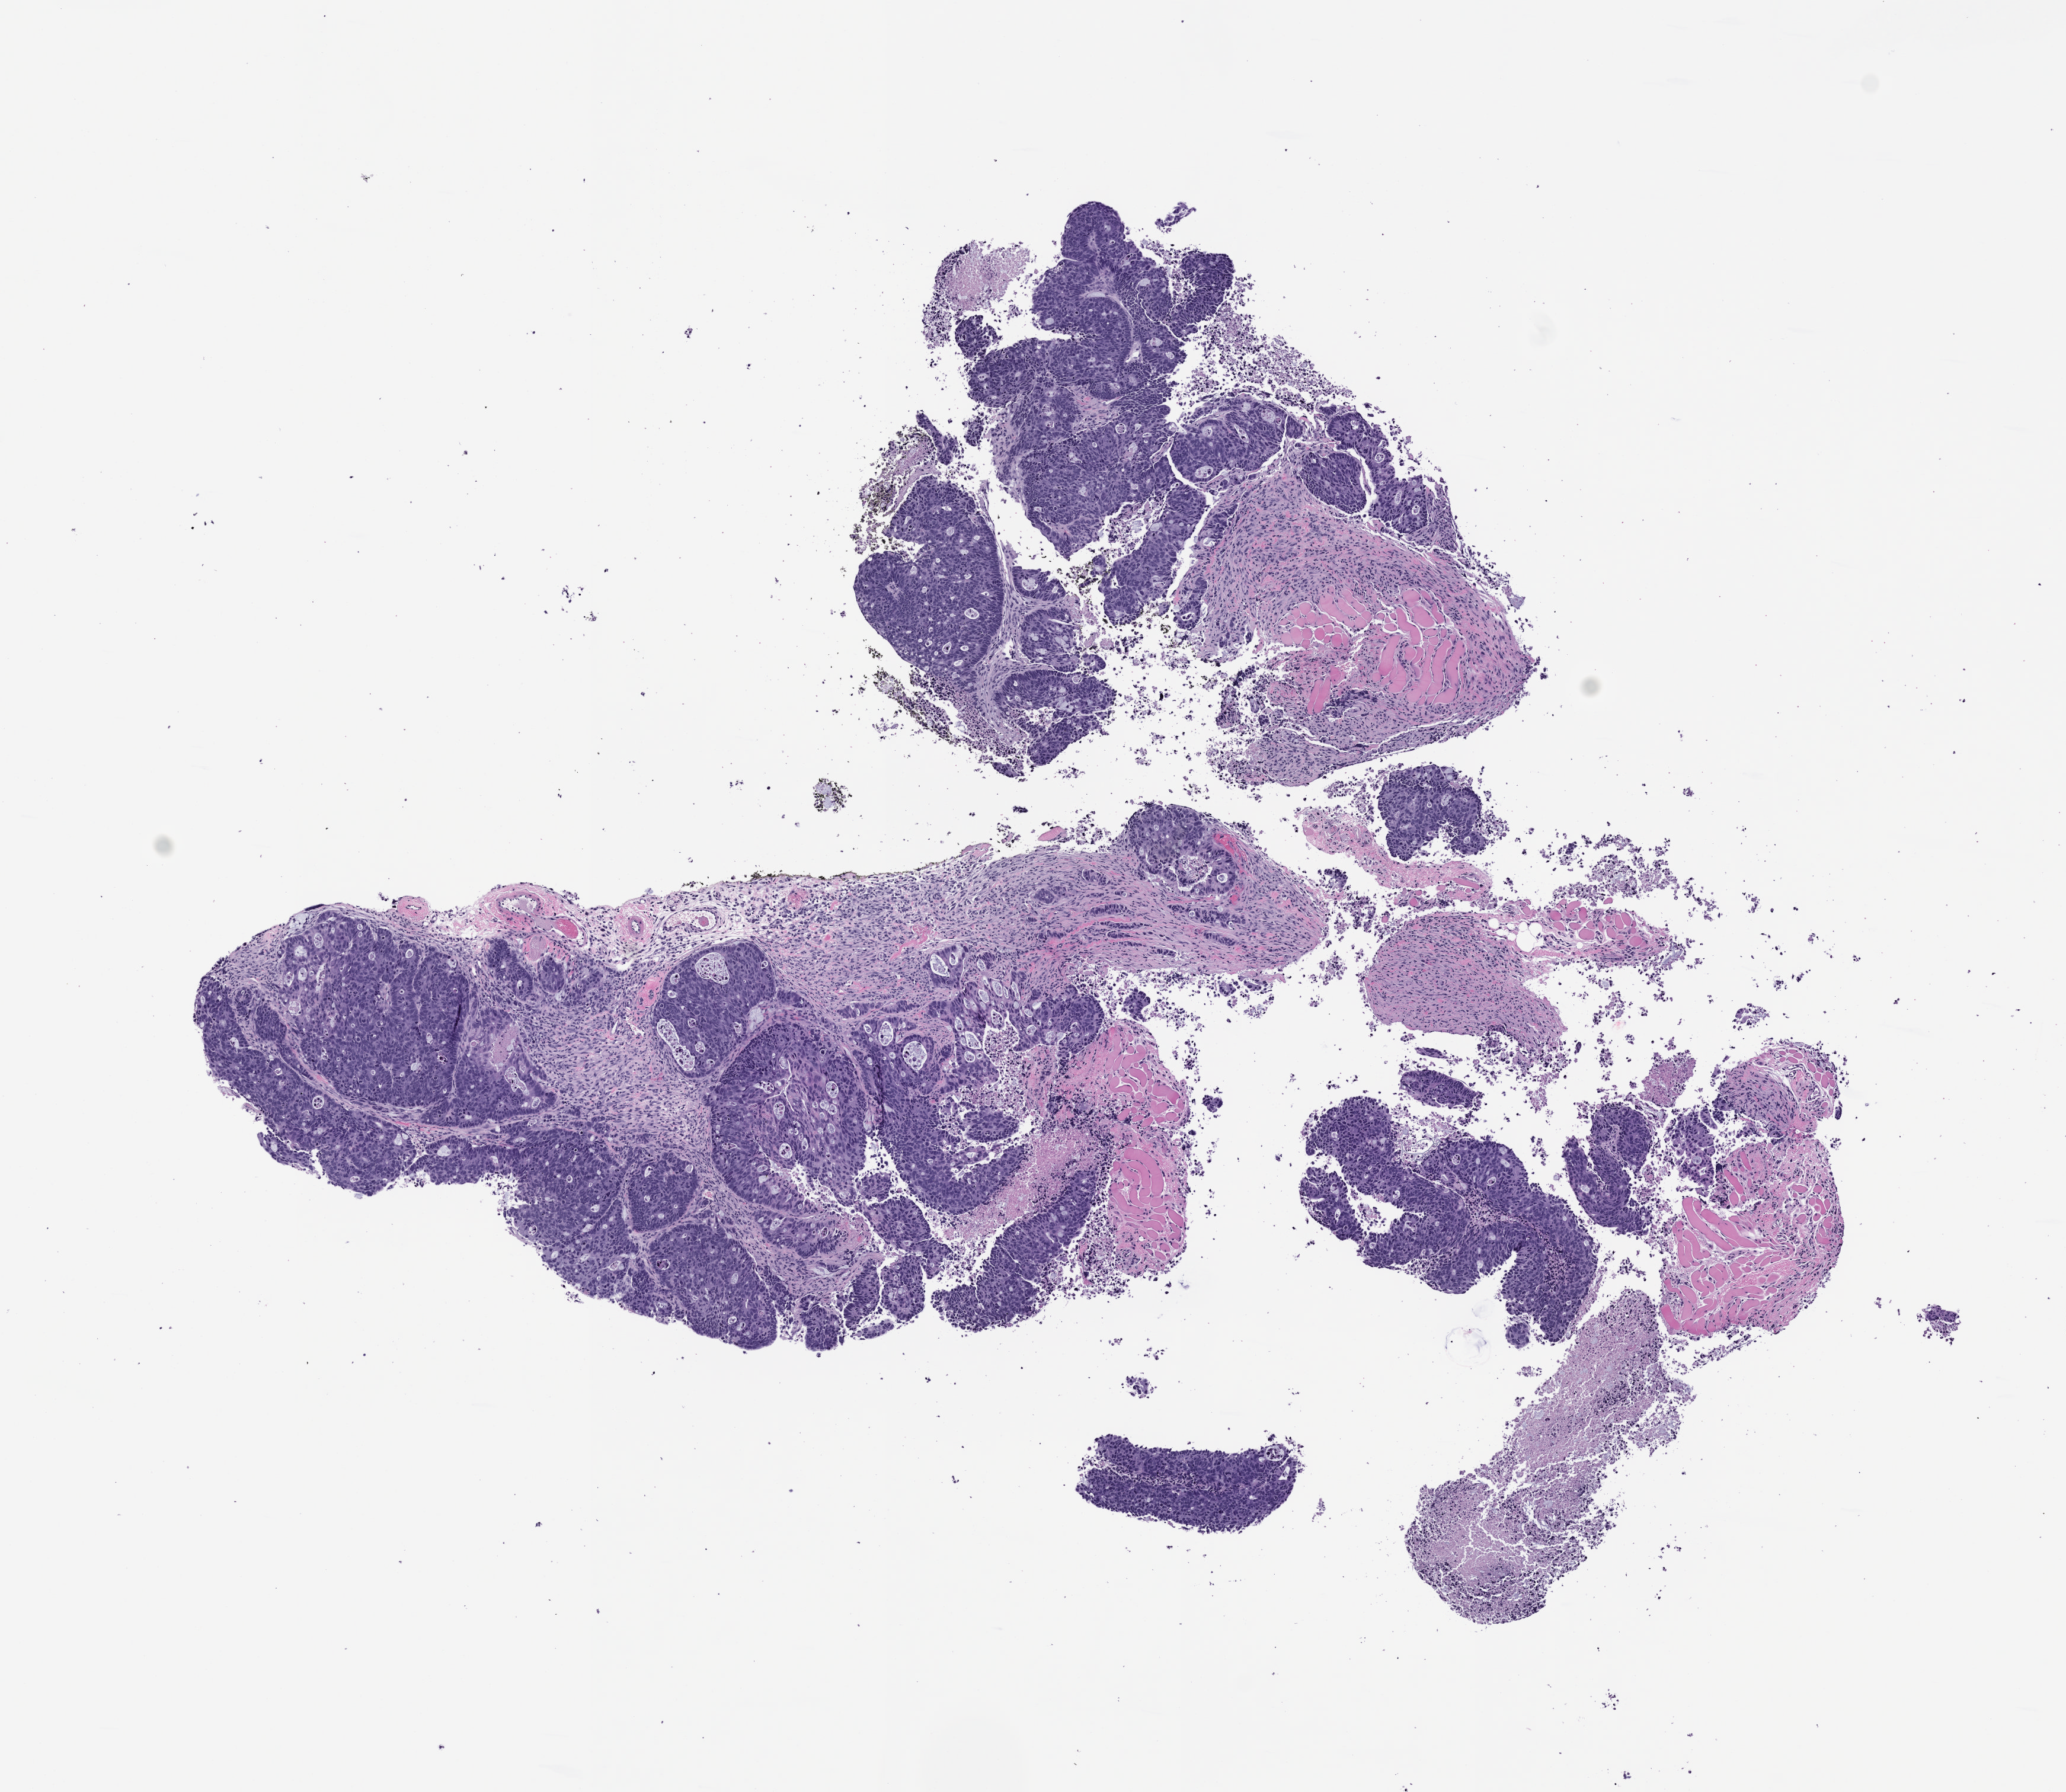
Hematoxylin and eosin (H&E) whole-slide image of a patient-derived xenograft (PDX) tumor grown in a mouse, passage 1 — low-resolution overview of the scanned area, about 7.0 x 6.1 mm. FFPE section. Originating tumor site category: rectum.
• originating patient diagnosis: Rectal Adenocarcinoma